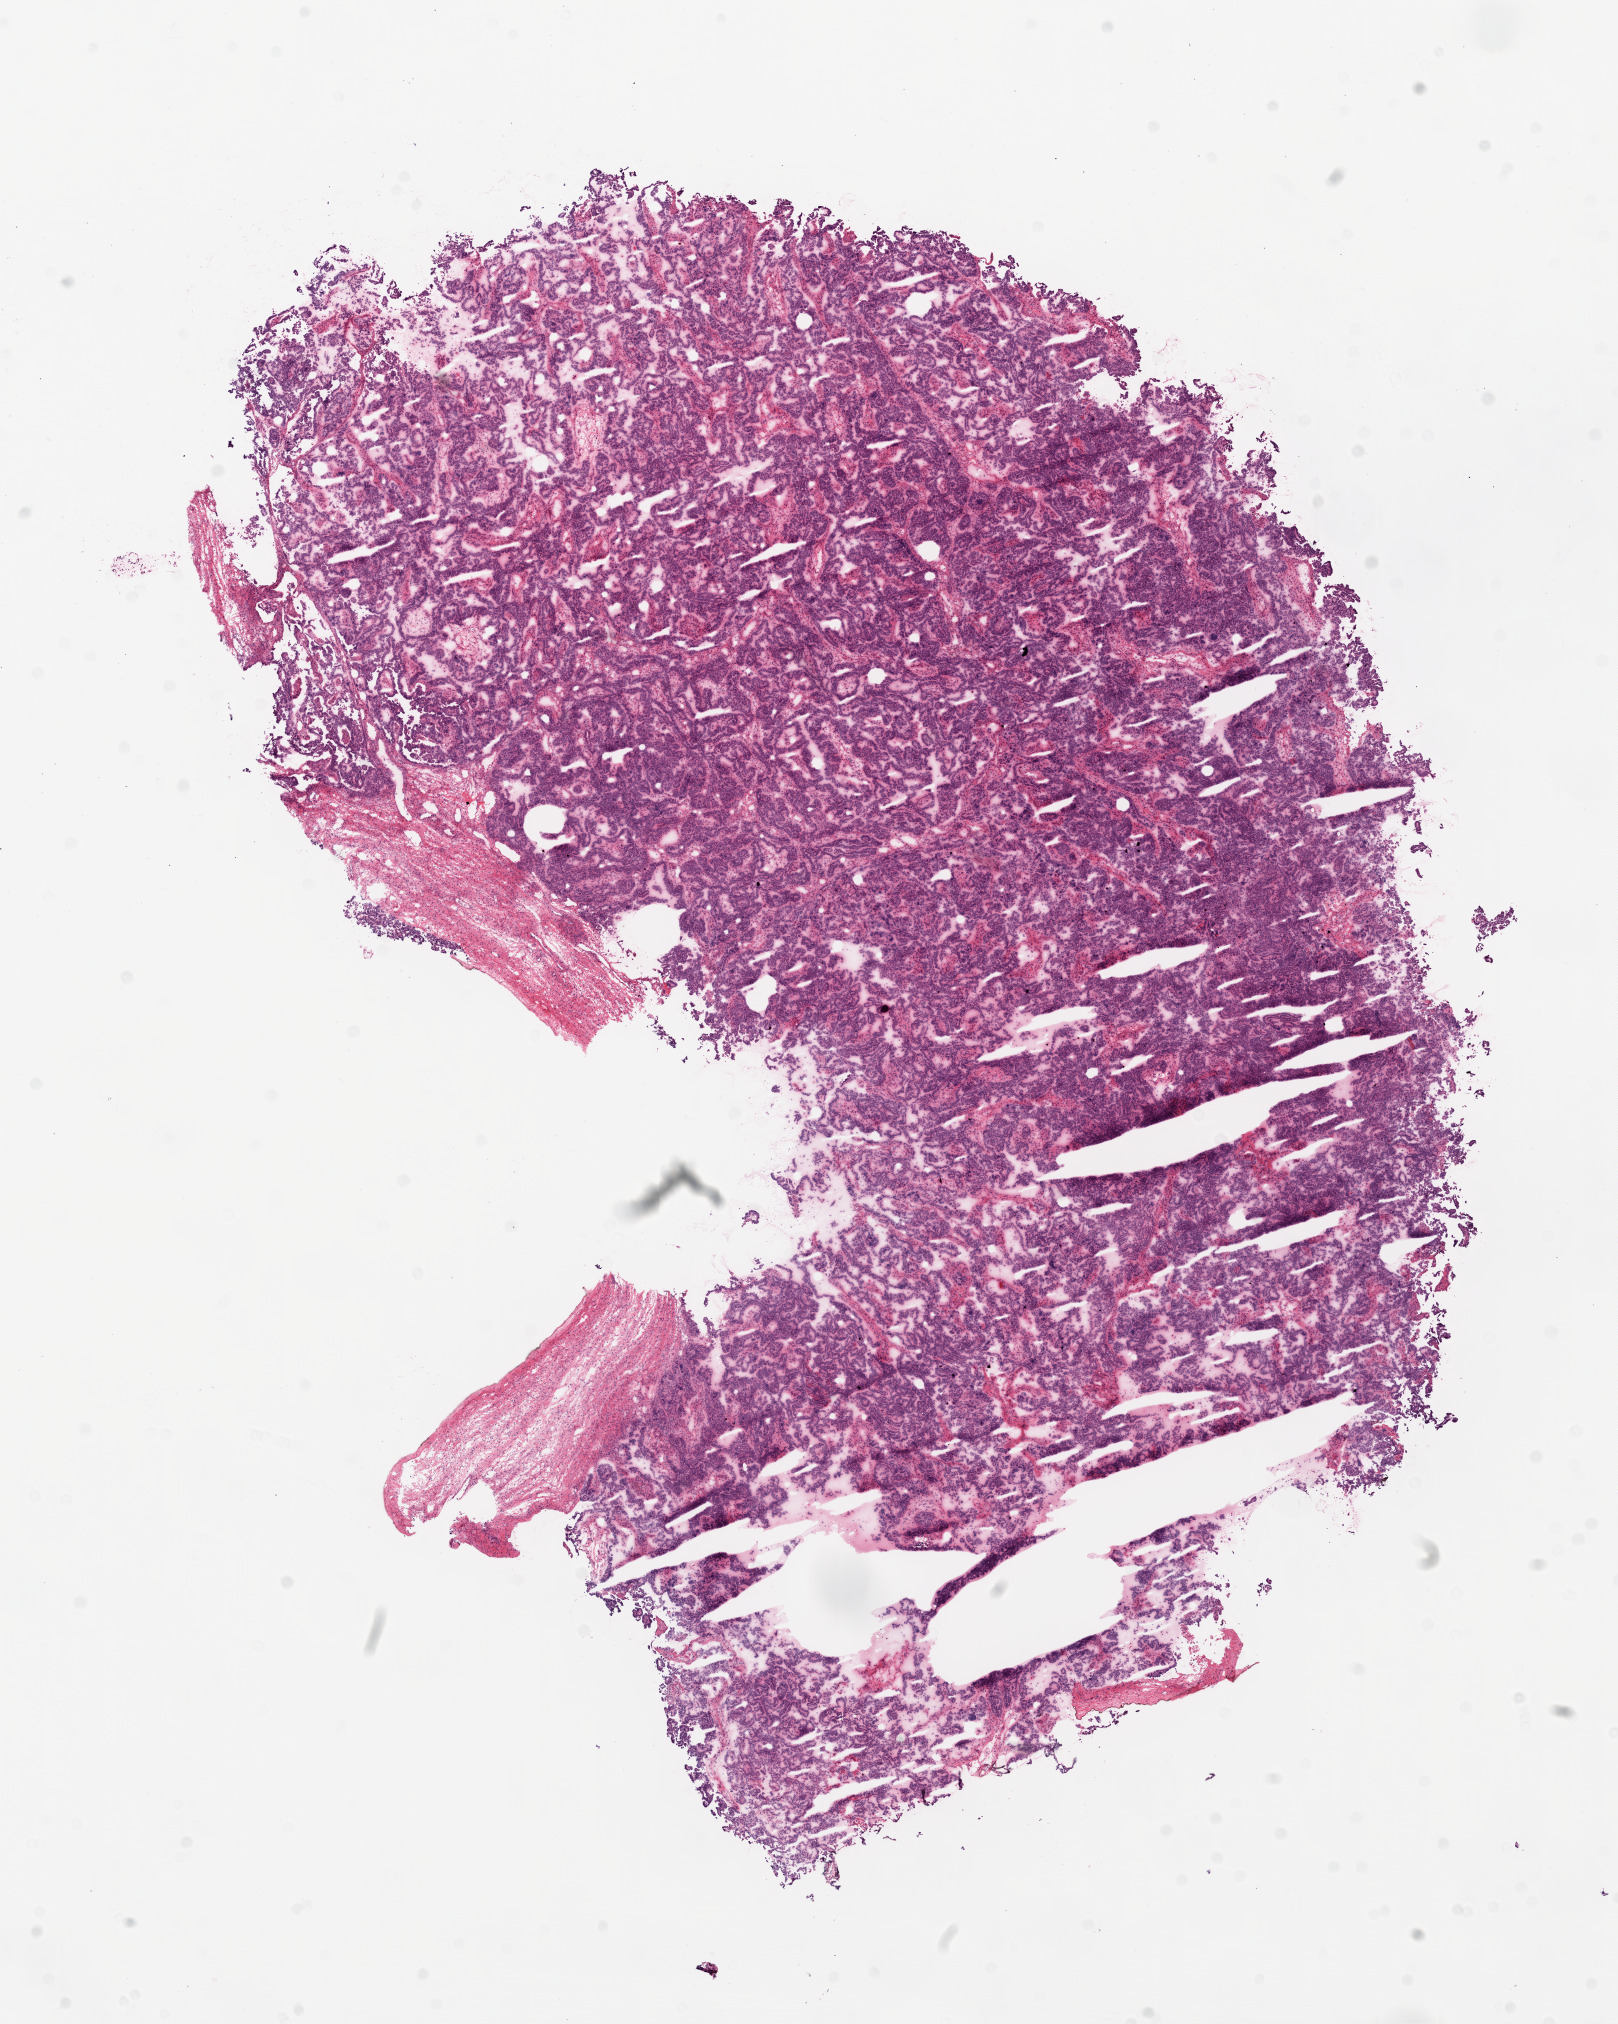
Whole-slide histology image, H&E — whole scanned area (about 13.1 x 16.3 mm) shown as a low-resolution overview, frozen section from the top of the tissue portion, sample: primary tumour, ovary. Patient: female, age at initial diagnosis 53 years. Histologic grade: G3 (poorly differentiated). Slide review estimates, as recorded: tumour cells 95%, tumour nuclei 99%, normal cells 0%, stromal cells 4%, necrosis 1%. Inflammatory infiltration, as recorded: lymphocyte infiltration 100%.
- diagnosis: Serous cystadenocarcinoma, NOS
- FIGO stage: IIIC